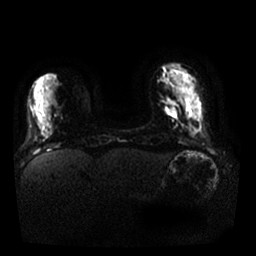
Breast MRI, one axial slice. Slice 7 of 25 in the series (ordered by position). Diffusion-weighted series; image 2 of 4 stored at this slice position (different b-values; order by instance number). 1.5 T. 4 mm slice thickness. 256 × 256 image matrix. Female patient.
Outlined on this slice (manually delineated by an expert):
- tumour on diffusion-weighted imaging: bounding box [x1, y1, x2, y2] px = [165, 107, 176, 113]